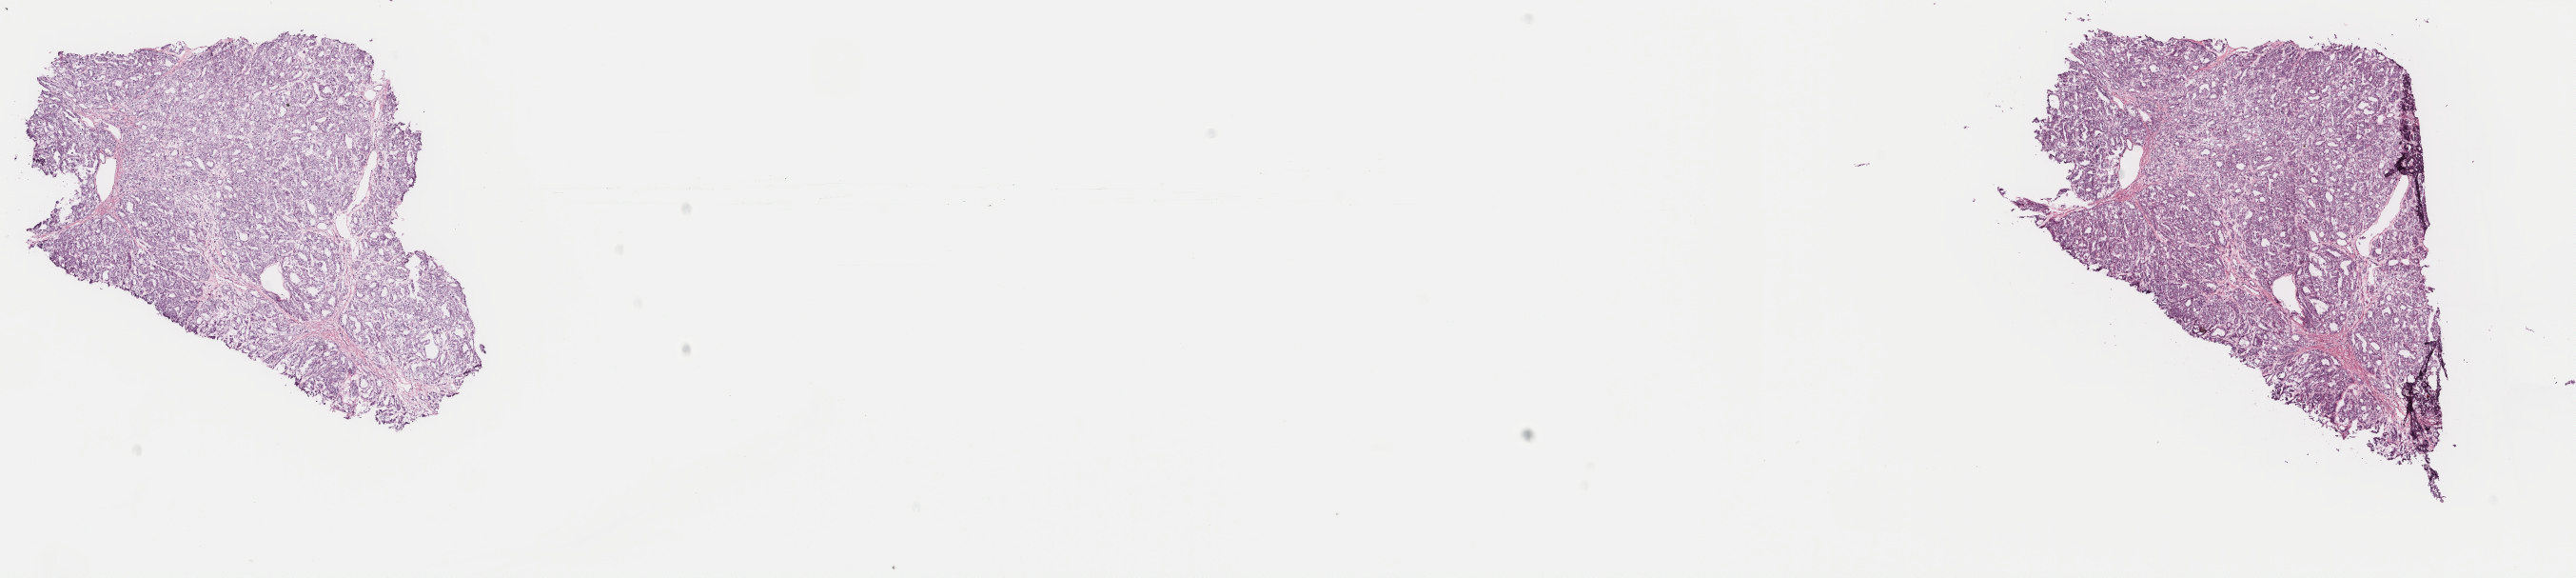
Whole-slide histology image, H&E, shown as a low-resolution overview of the whole scanned area (about 21.5 x 4.8 mm); frozen section from the top of the tissue portion; primary tumour sample from the kidney. Patient: female, age at initial diagnosis 51 years. Composition of this section per pathologist review: tumour cells 90%, tumour nuclei 85%, normal cells 0%, stromal cells 10%, necrosis 0%. Infiltration values recorded for this section: lymphocyte infiltration 0%, monocyte infiltration 0%, neutrophil infiltration 0%.
AJCC pathologic stage: I (7th edition). Histologic diagnosis: Renal cell carcinoma, chromophobe type. Laterality: left.